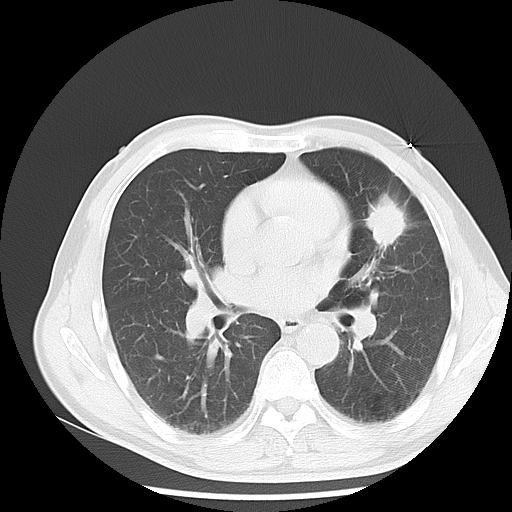
Chest CT, one axial slice; slice 7 of 13 in the series (ordered by position); 120 kVp; lung window (W 1500 / L -600 HU); 512 × 512 image matrix, field of view 350 × 350 mm. Patient: male, 54 years. Case-level facts recorded for this patient, not image findings: clinical TNM (as recorded): T1c N0 M0.
Outlined on this slice (rectangle marked by the reading radiologist):
- lung tumour (recorded histology: adenocarcinoma): box from (x=356, y=188) to (x=410, y=251) px